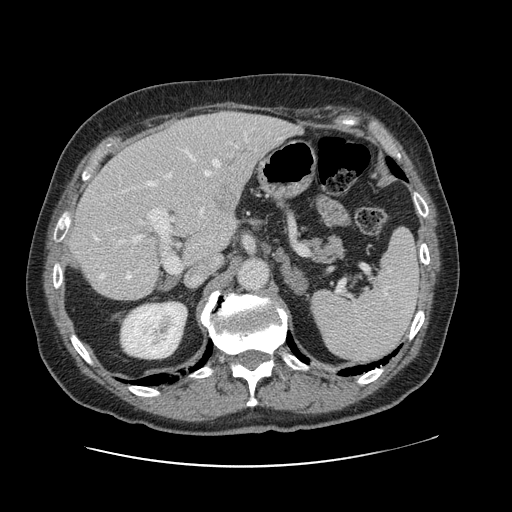
Contrast-enhanced abdominal CT, one axial slice; slice 71 of 138 in the series (ordered by position); 120 kVp; intravenous contrast given; soft-tissue window (W 400 / L 40 HU); 2.5 mm slice thickness; 512 × 512 image matrix, field of view 402 × 402 mm. Male patient, age 71 years. Case-level facts recorded for this patient, not image findings: diagnosis: colorectal cancer liver metastases, imaged before liver resection; multiple liver metastases: no; largest metastasis: 3.3 cm; disease in both lobes: no.
Outlined on this slice (manually delineated by an expert):
- hepatic veins: bounding box (x1, y1, x2, y2) in pixels: (94, 151, 223, 279)
- liver: (71, 113, 295, 300)
- planned liver remnant (the part of the liver to remain after resection): (71, 147, 226, 300)
- portal vein (with intrahepatic branches): (117, 133, 247, 273)
- liver metastasis: (211, 185, 239, 215)